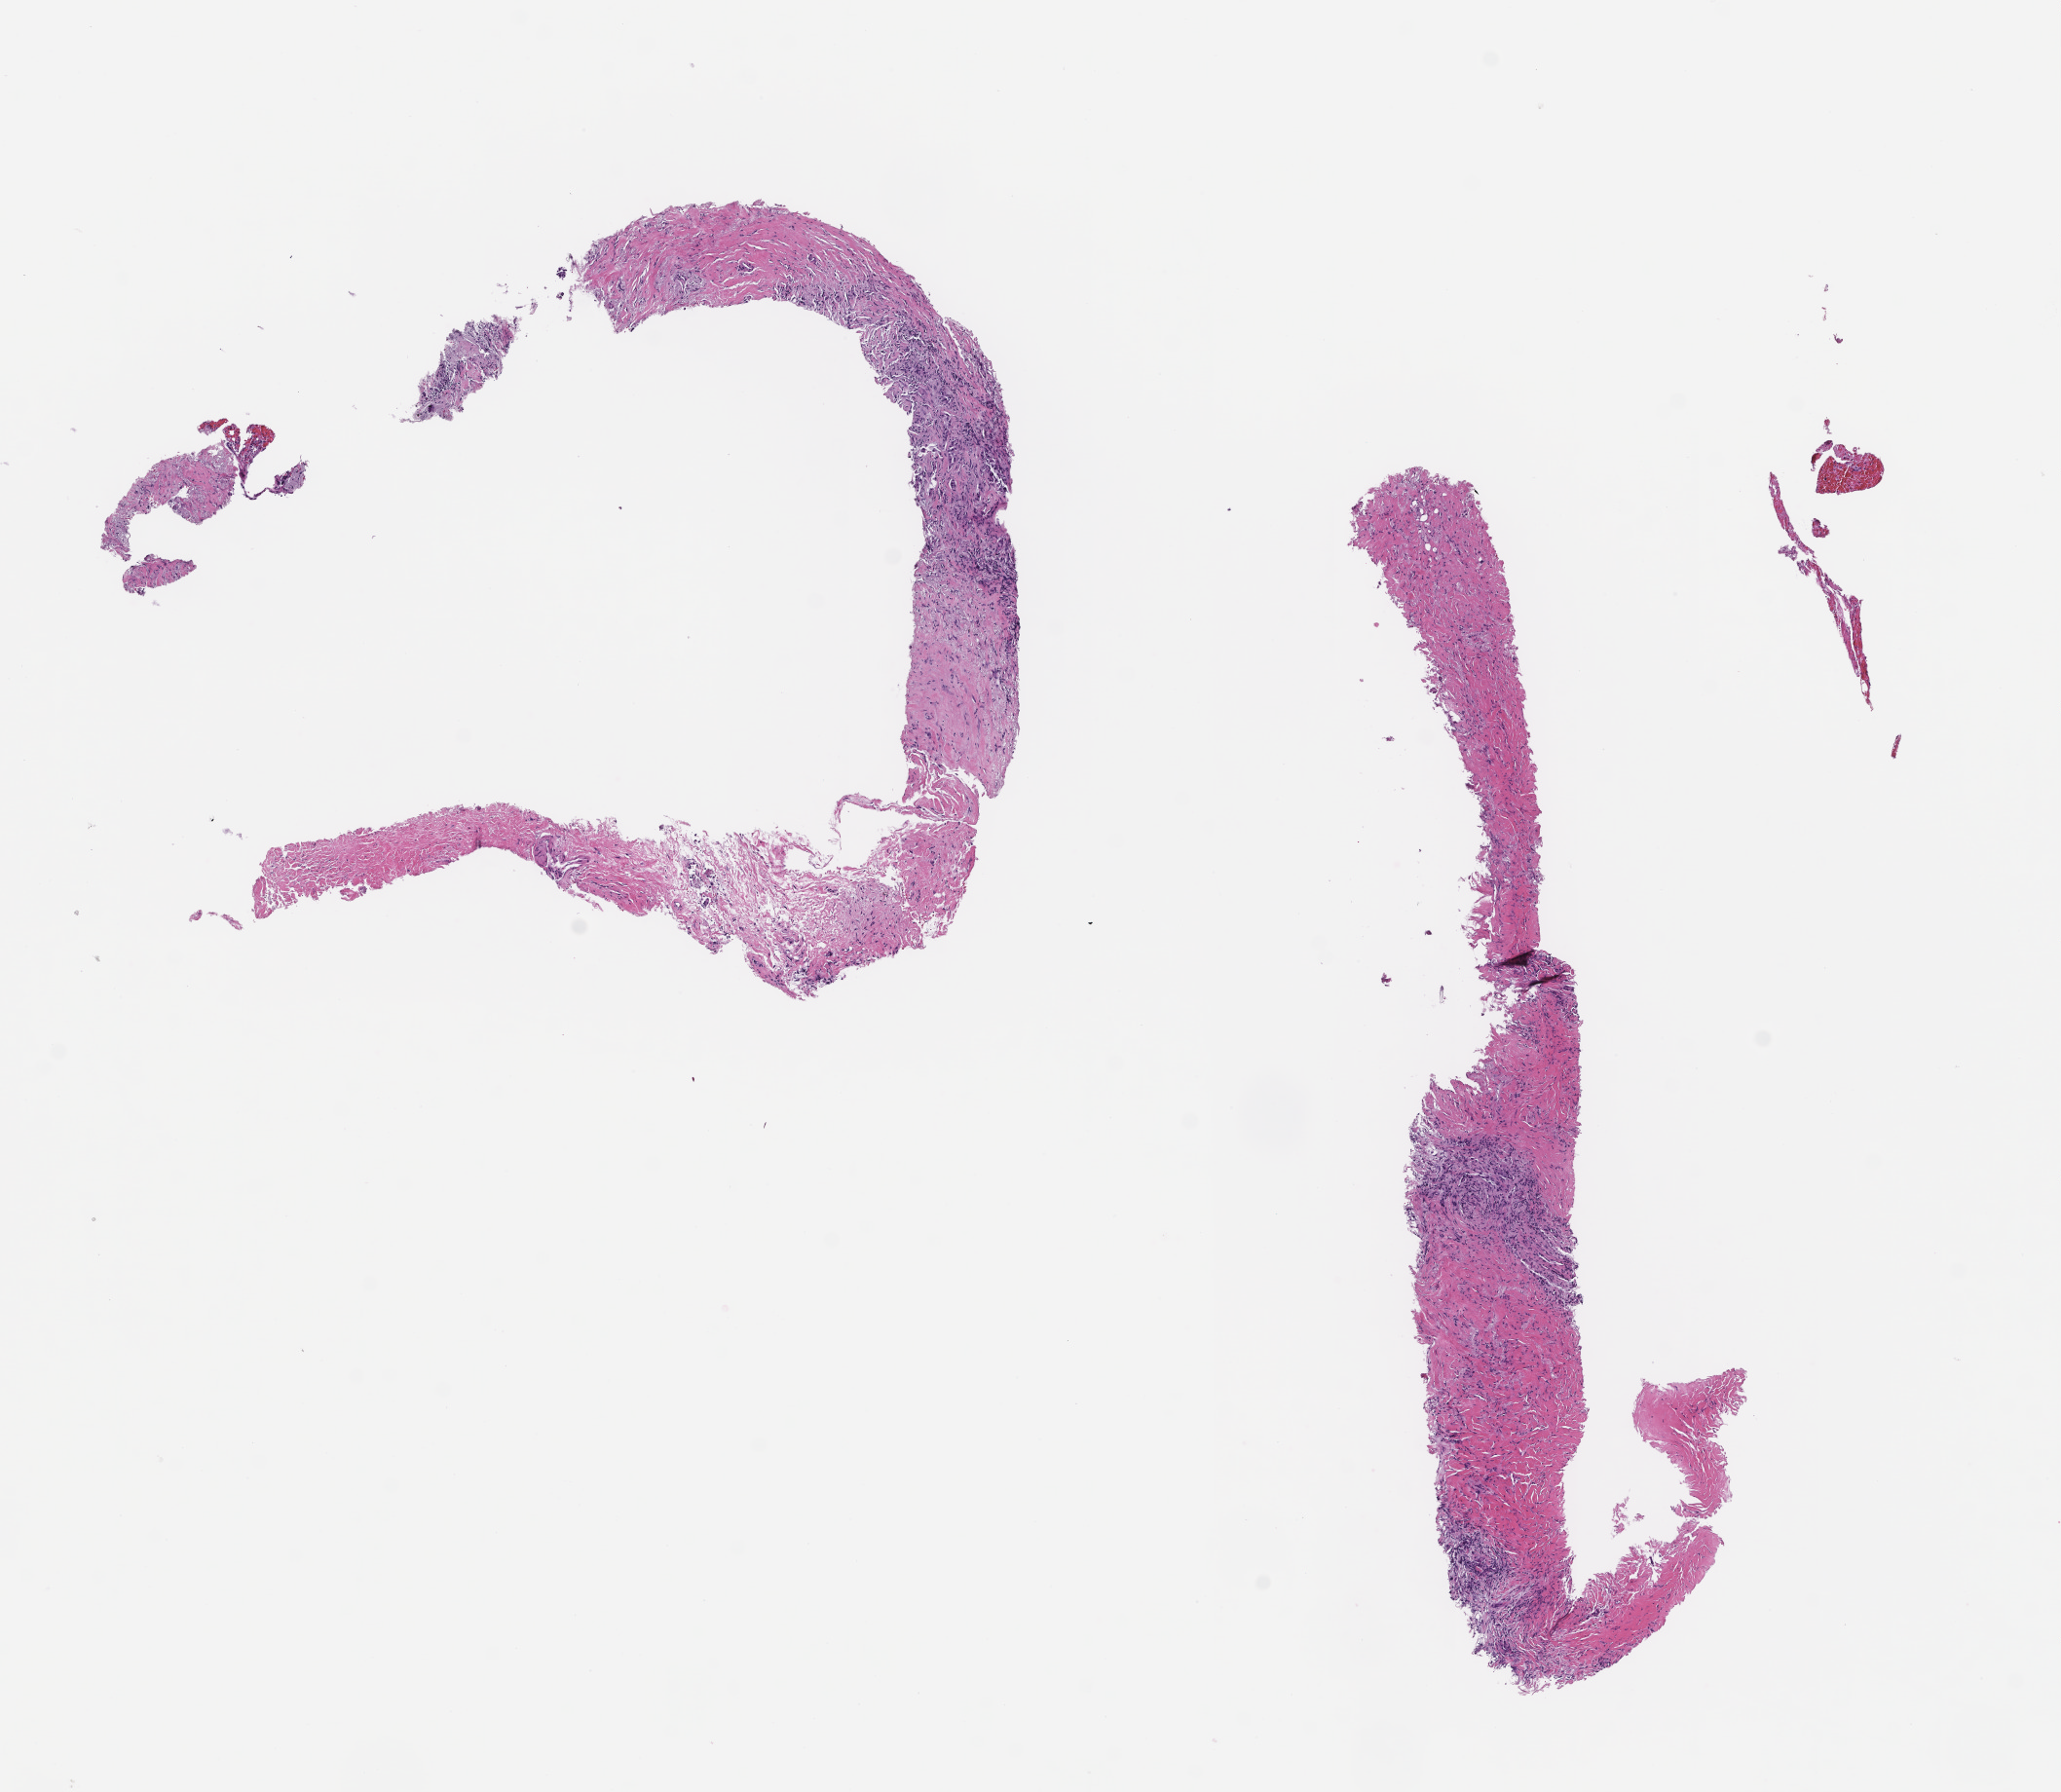
Digitized hematoxylin and eosin (H&E)-stained section, whole scanned area (about 8.5 x 7.4 mm) shown as a low-resolution overview; formalin-fixed paraffin-embedded section; tissue site: lung; archival tissue. Patient: female.
This section: primary tumor. Diagnosis: Non-Small Cell Lung Carcinoma.